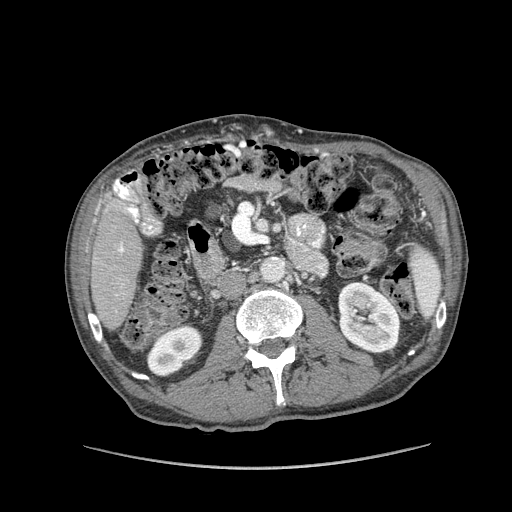
Contrast-enhanced abdominal CT (liver protocol), one axial slice; slice 25 of 162 in the series (ordered by position); soft-tissue window (W 400 / L 40 HU); 512 × 512 image matrix, field of view 400 × 400 mm. Case-level facts recorded for this patient, not image findings: diagnosis: hepatocellular carcinoma (patient treated with transarterial chemoembolisation; whether this scan precedes or follows treatment is not stated here); TNM stage (as recorded): Stage-IIIA; Child-Pugh class: A; tumour nodularity: multinodular; tumour size: 9.9 cm.
Annotated regions visible in this slice (semi-automatic segmentation, software-assisted and operator-edited):
- liver parenchyma outside the tumour (the mass and vessels are separate outlines, so this box may not span the whole liver): bounding box [x1, y1, x2, y2] px = [90, 192, 142, 330]
- liver vessels: [118, 243, 124, 253]